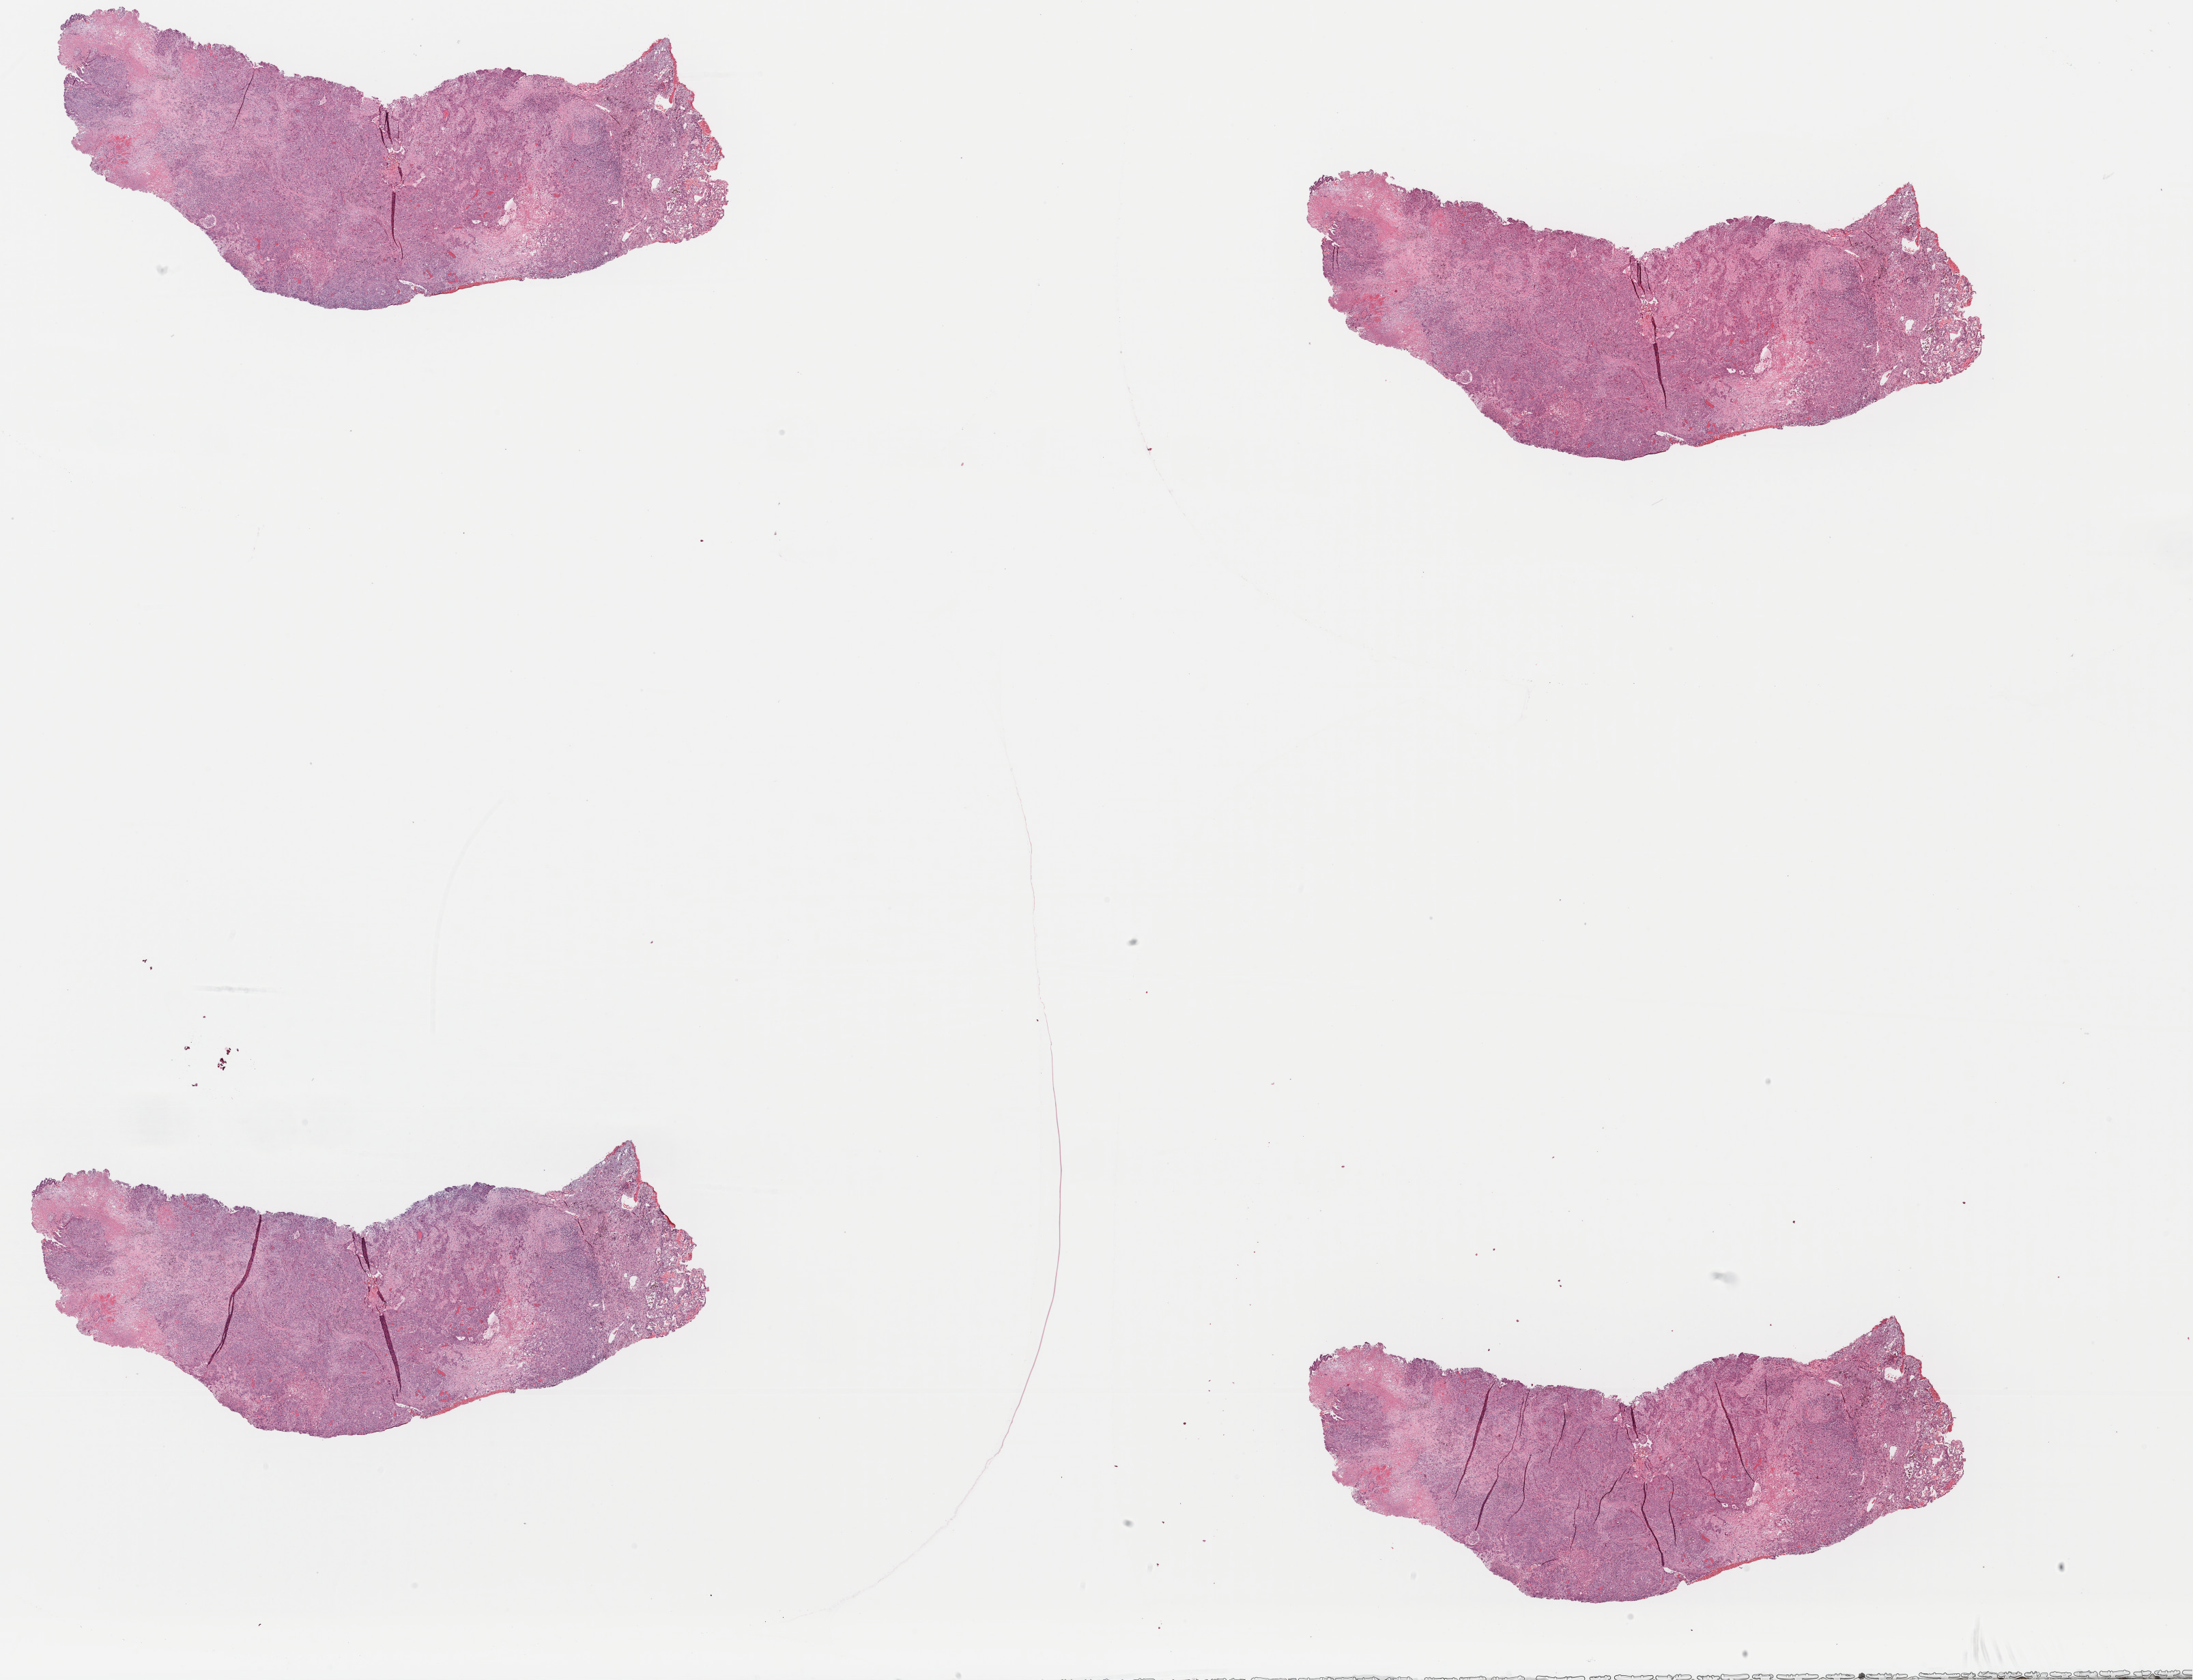
H&E-stained whole-slide image — shown as a low-resolution overview of the whole scanned area (about 25.4 x 19.4 mm, slide scanned at 40x); formalin-fixed paraffin-embedded (FFPE) diagnostic section; sample: primary tumour, lung. Male, age 73 years at initial diagnosis.
• diagnosis: Adenocarcinoma, NOS (upper lobe, lung)
• AJCC pathologic stage: IA (7th edition)
• laterality: left